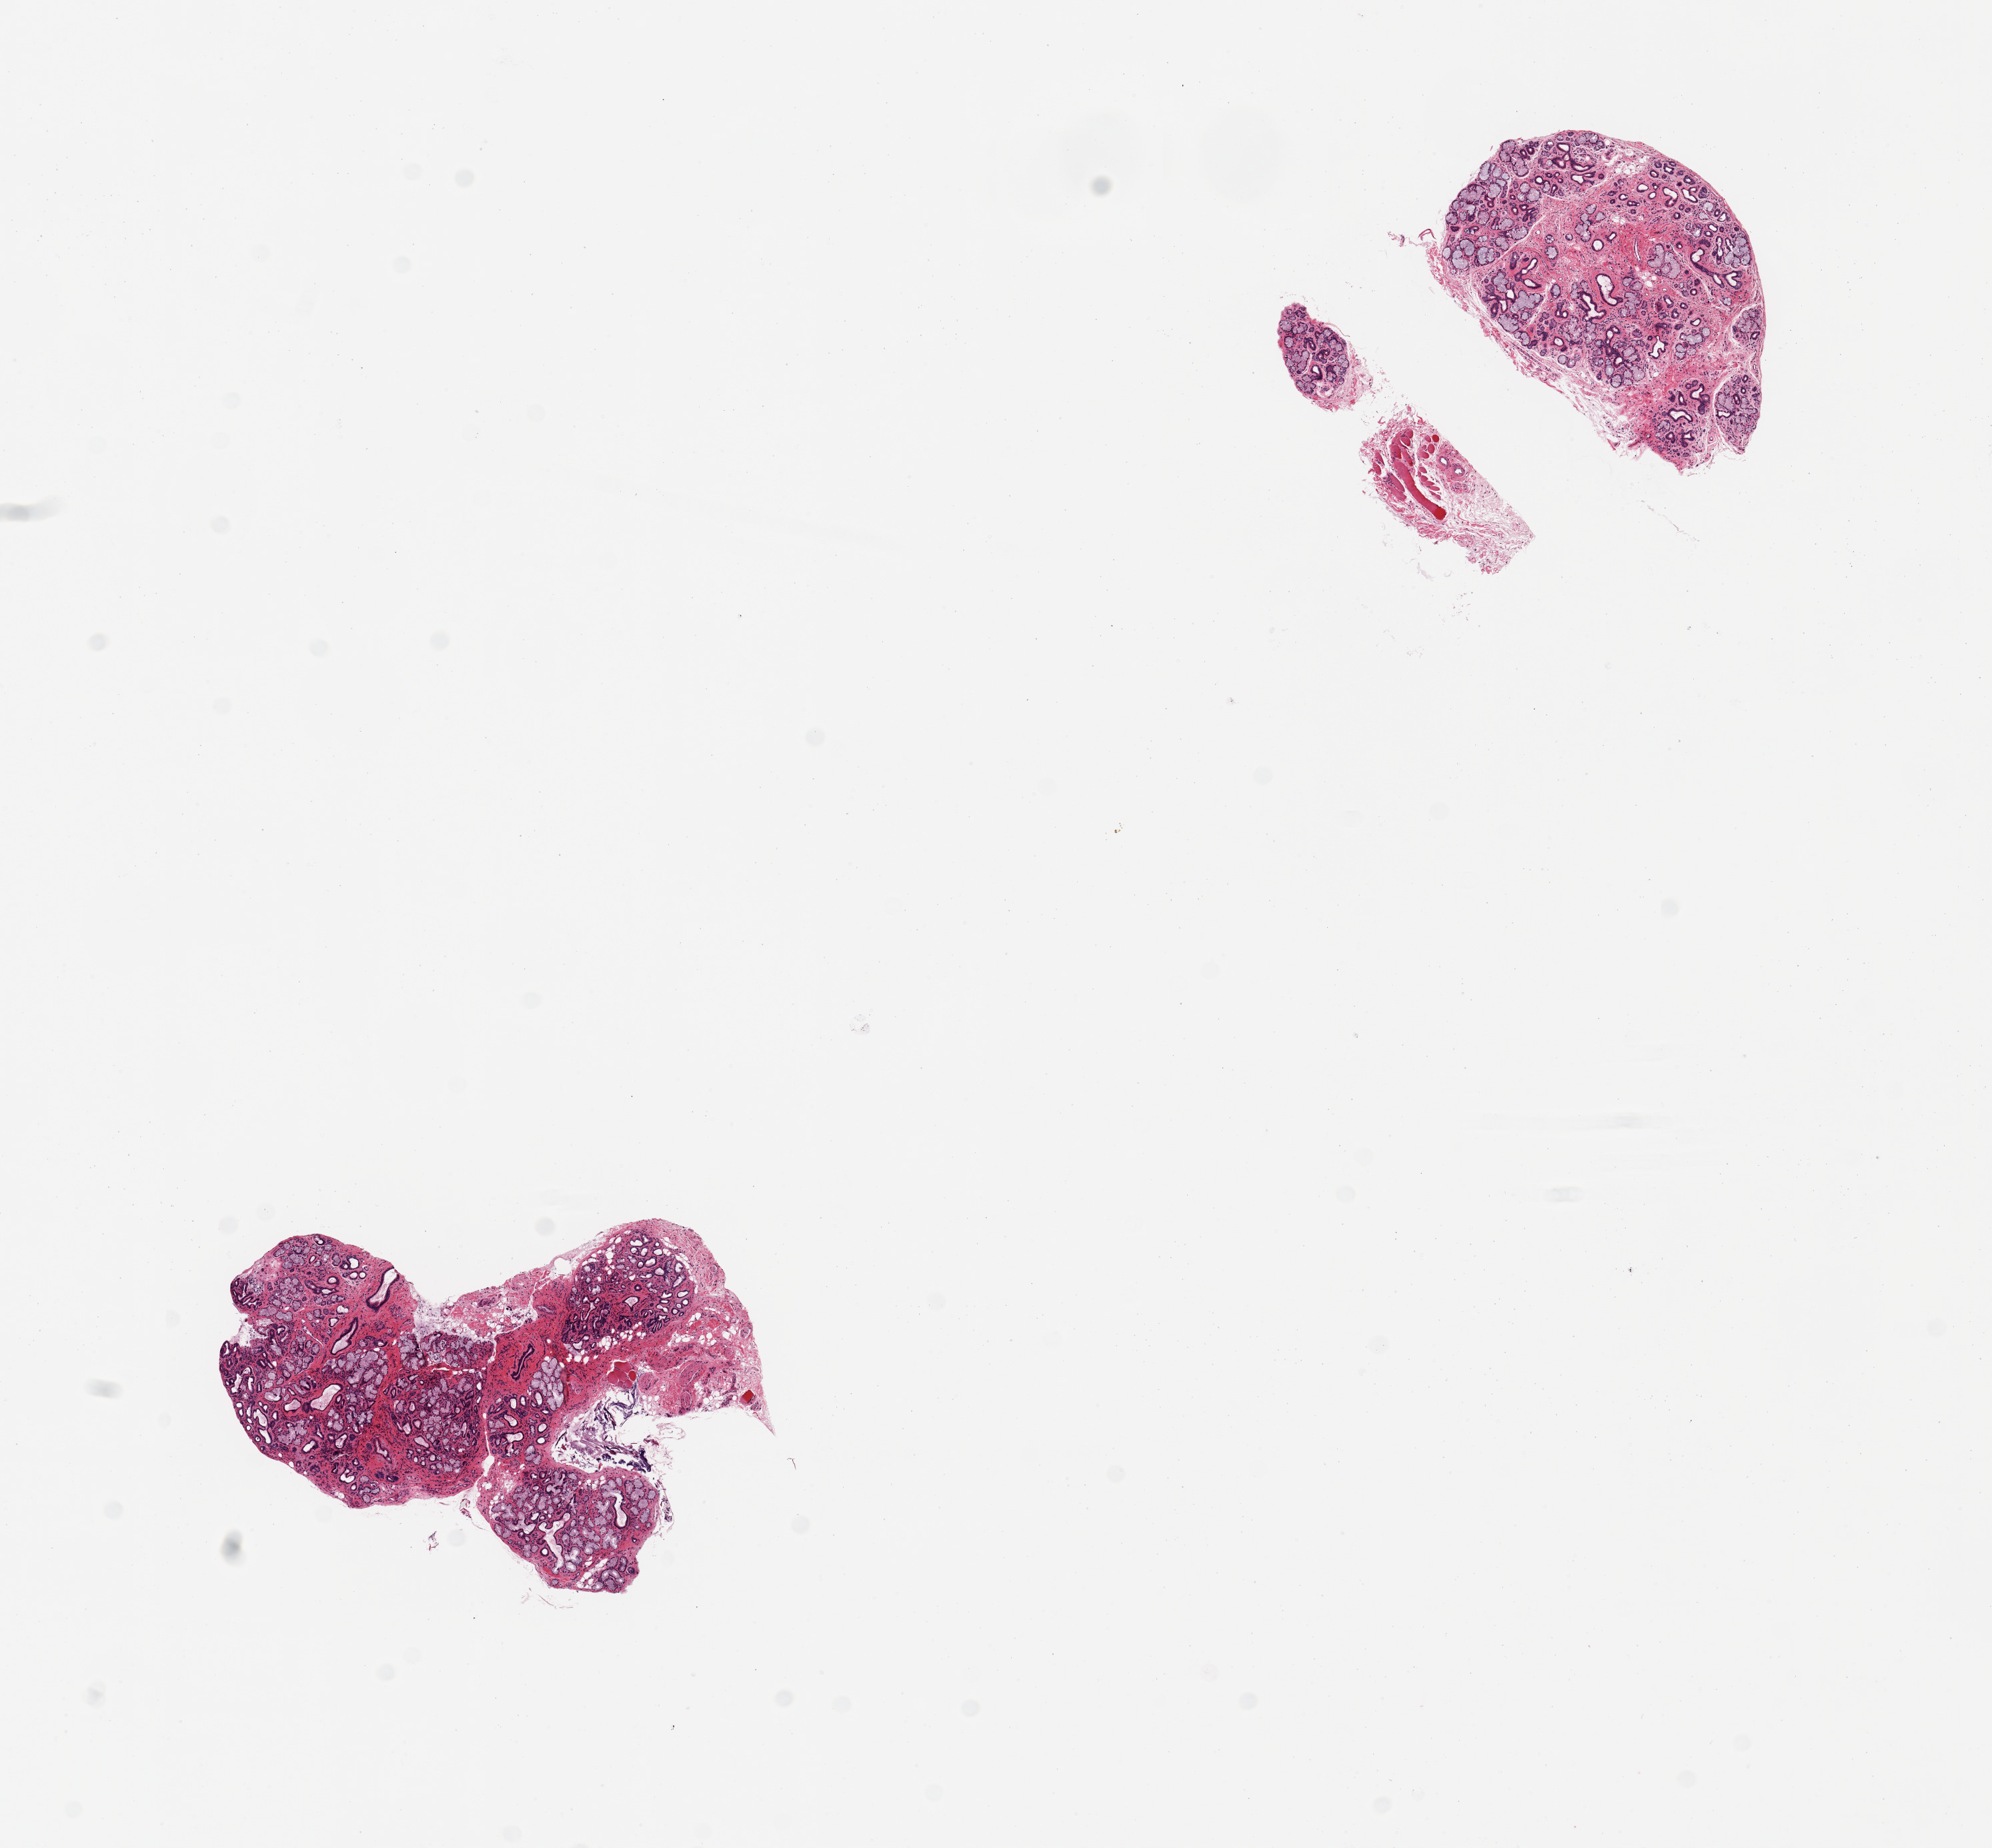
Hematoxylin and eosin (H&E) whole-slide image, brightfield, low-resolution overview of the scanned area, about 11.8 x 11.0 mm (from a 20x scan). PAXgene-fixed, paraffin-embedded tissue. Target tissue: minor salivary gland. Donor tissue sample. Donor sex: male.
Reviewer comment on this tissue sample: 2 pieces, ~90& glandular parenchyma.